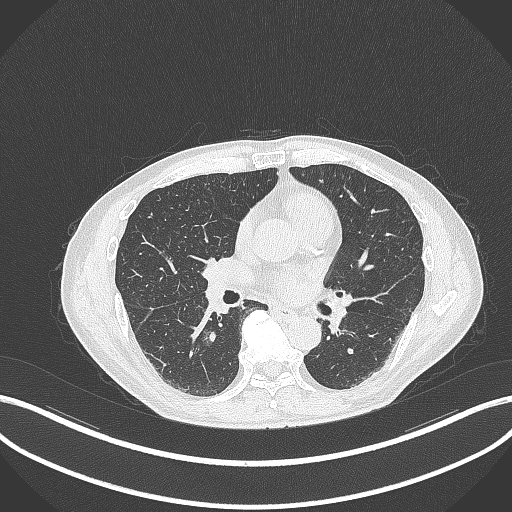
Chest CT, one axial slice. Lung window (W 1500 / L -600 HU). 512 × 512 image matrix, field of view 400 × 400 mm. Male patient, age 61 years. Case-level facts recorded for this patient, not image findings: clinical TNM (as recorded): T1c N0 M0.
Structures marked on this image (bounding box drawn by a radiologist):
- lung tumour (recorded histology: adenocarcinoma): box from (x=200, y=328) to (x=219, y=350) px